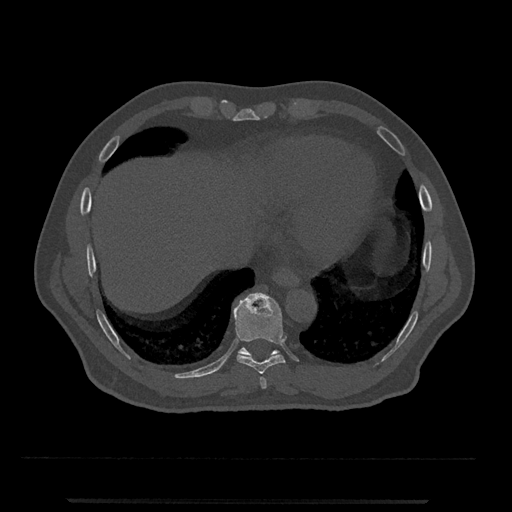
CT including the spine, one axial slice. Slice 560 of 797 in the series (ordered by position). 120 kVp. Bone window (W 1800 / L 400 HU). 512 × 512 image matrix. Patient: male, 63 years. Case-level facts recorded for this patient, not image findings: primary cancer: prostate.
Annotated regions visible in this slice (semi-automatically segmented with operator editing):
- T10 vertebra: bounding box <238,347,280,358> (left, top, right, bottom; pixels)
- T8 vertebra: <259,377,267,389>
- T9 vertebra: <233,293,286,374>